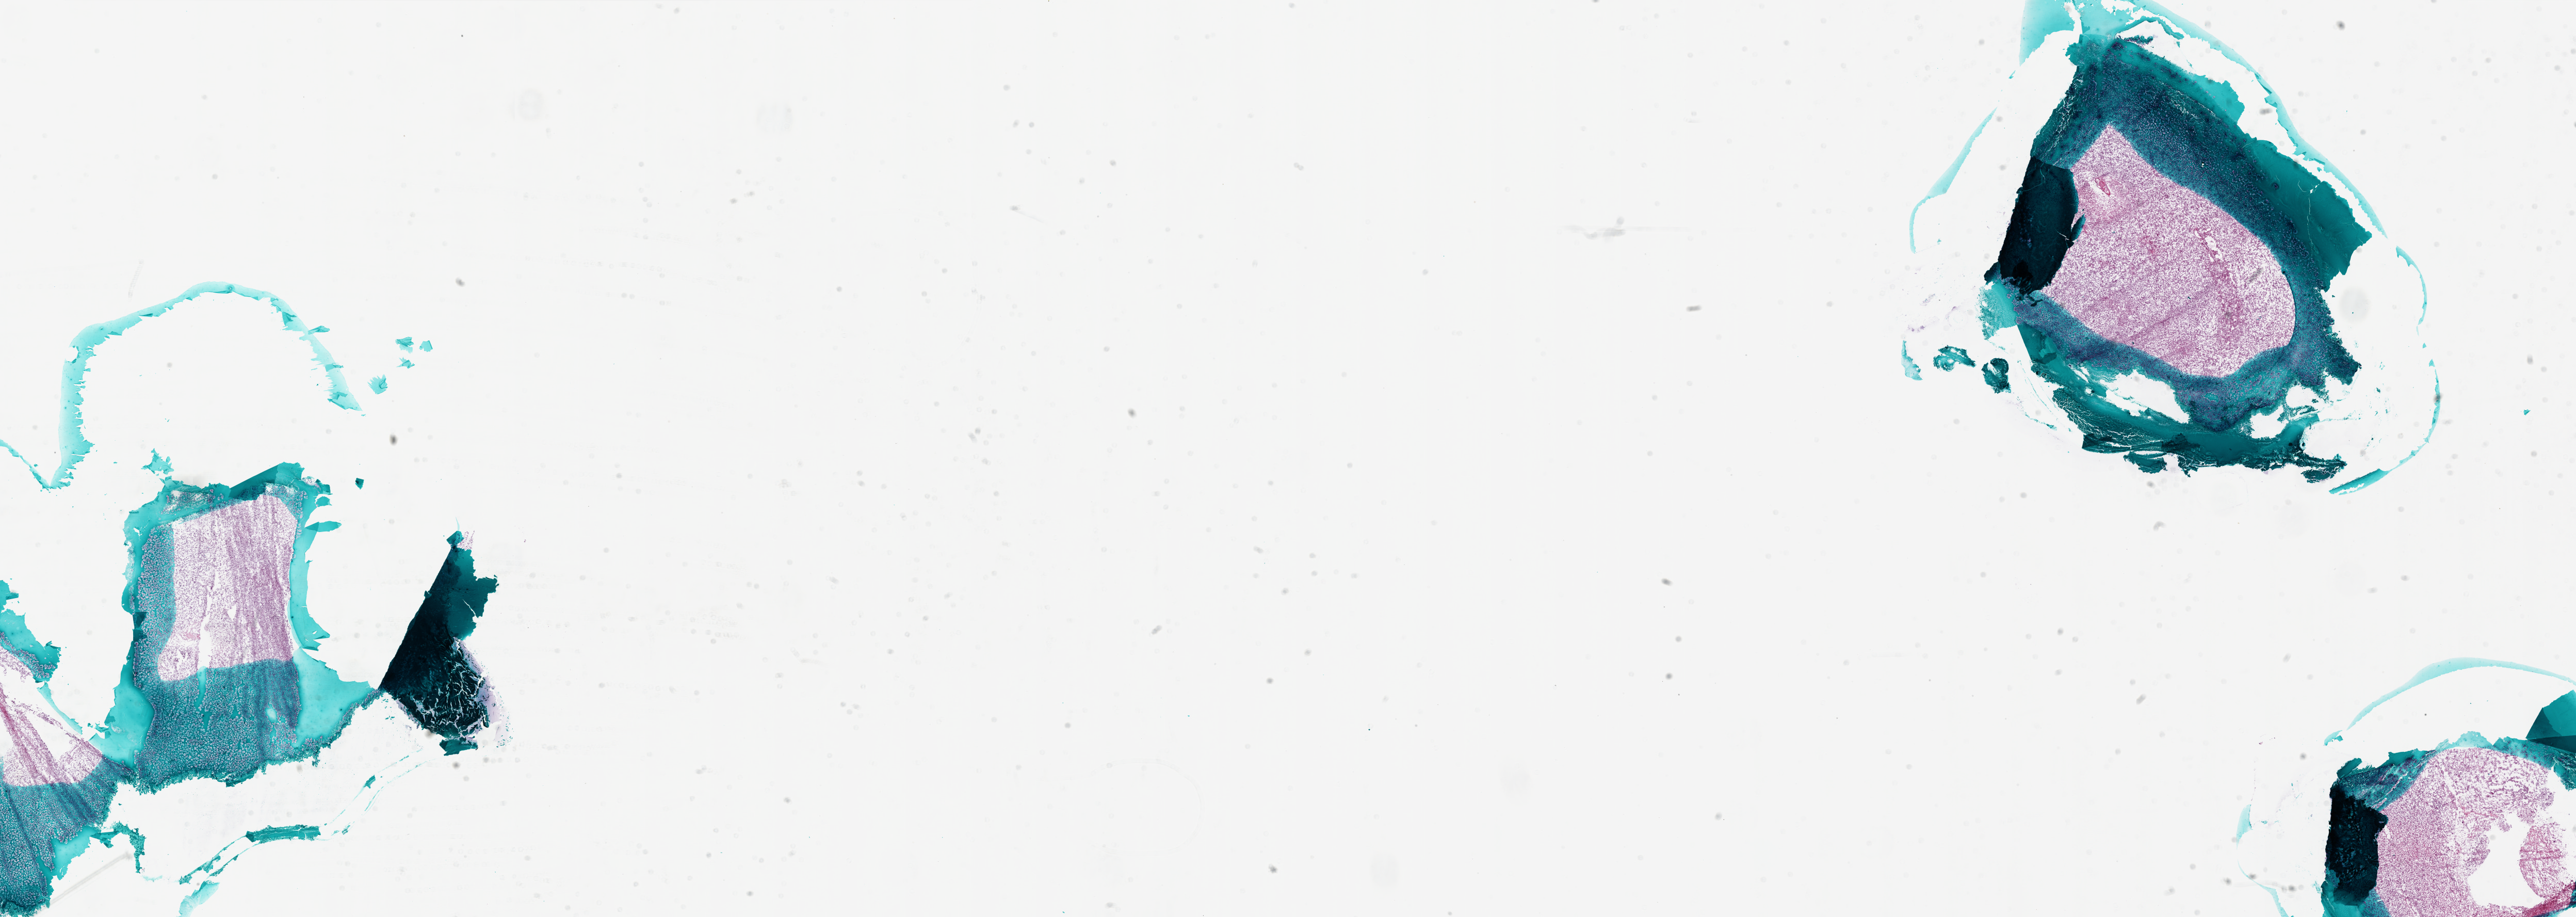
Digitized Hematoxylin and eosin (H&E) stained tissue section (whole slide), shown as a low-resolution overview of the whole scanned area (about 40.0 x 14.2 mm). Frozen section. Brain, primary tumour sample. Male, age 50 years at initial diagnosis. Slide review estimates, as recorded: tumour cells 90%, tumour nuclei 100%, normal cells 0%, stromal cells 0%, necrosis 10%.
* pathologic diagnosis: Glioblastoma